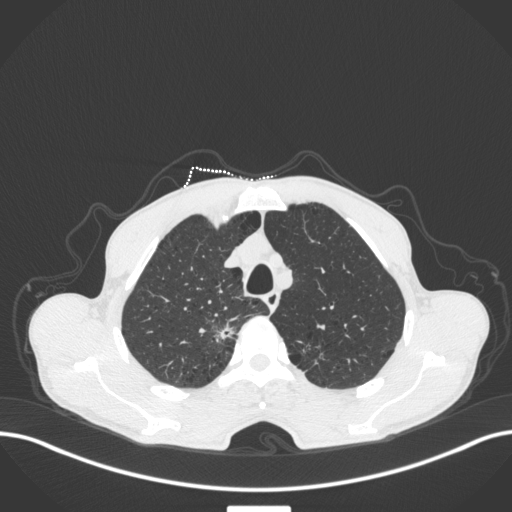
Chest CT, one axial slice; slice 347 of 445 in the series (ordered by position); lung window (W 1500 / L -600 HU); 1 mm slice thickness; 512 × 512 image matrix. Patient: male, 70 years. From the clinical record (not read from this slice): clinical TNM (as recorded): T1a N0 M0; histopathological grade: G1-2.
Outlined on this slice (bounding box drawn by a radiologist):
- lung tumour (recorded histology: adenocarcinoma): box from (x=212, y=320) to (x=240, y=346) px